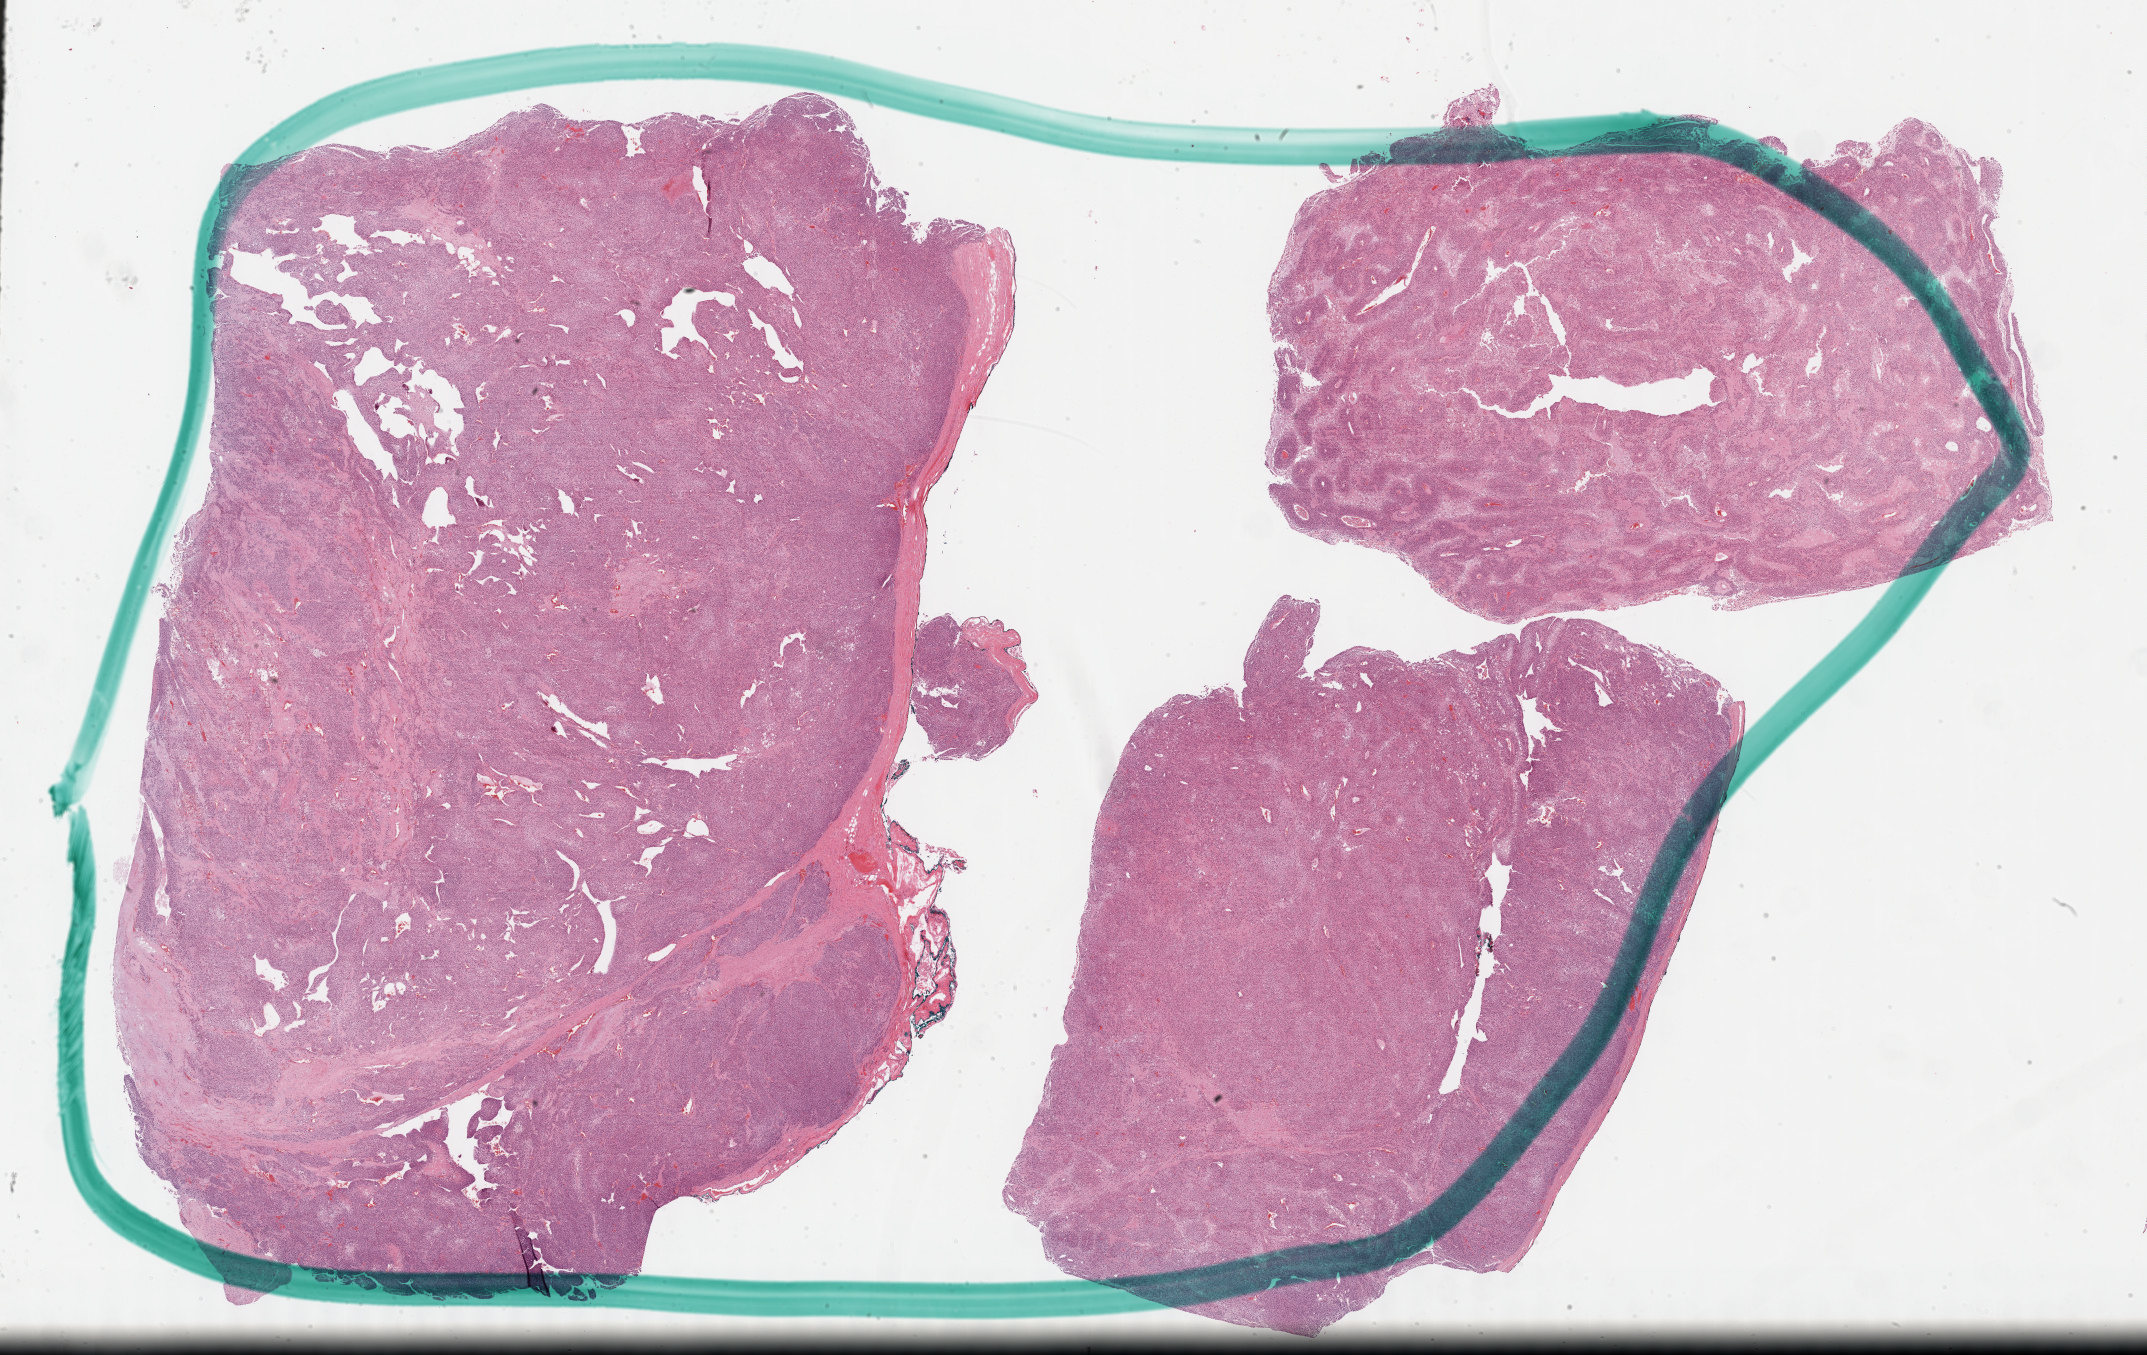
Hematoxylin and eosin (H&E) stained whole-slide image, whole scanned area (about 34.7 x 21.9 mm) shown as a low-resolution overview; formalin-fixed paraffin-embedded (FFPE) diagnostic section; adrenal cortex, primary tumour sample. Female, age 59 years at initial diagnosis.
Lymph nodes positive (case pathology): 0 of 20 examined. Pathologic diagnosis: Adrenal cortical carcinoma (cortex of adrenal gland).